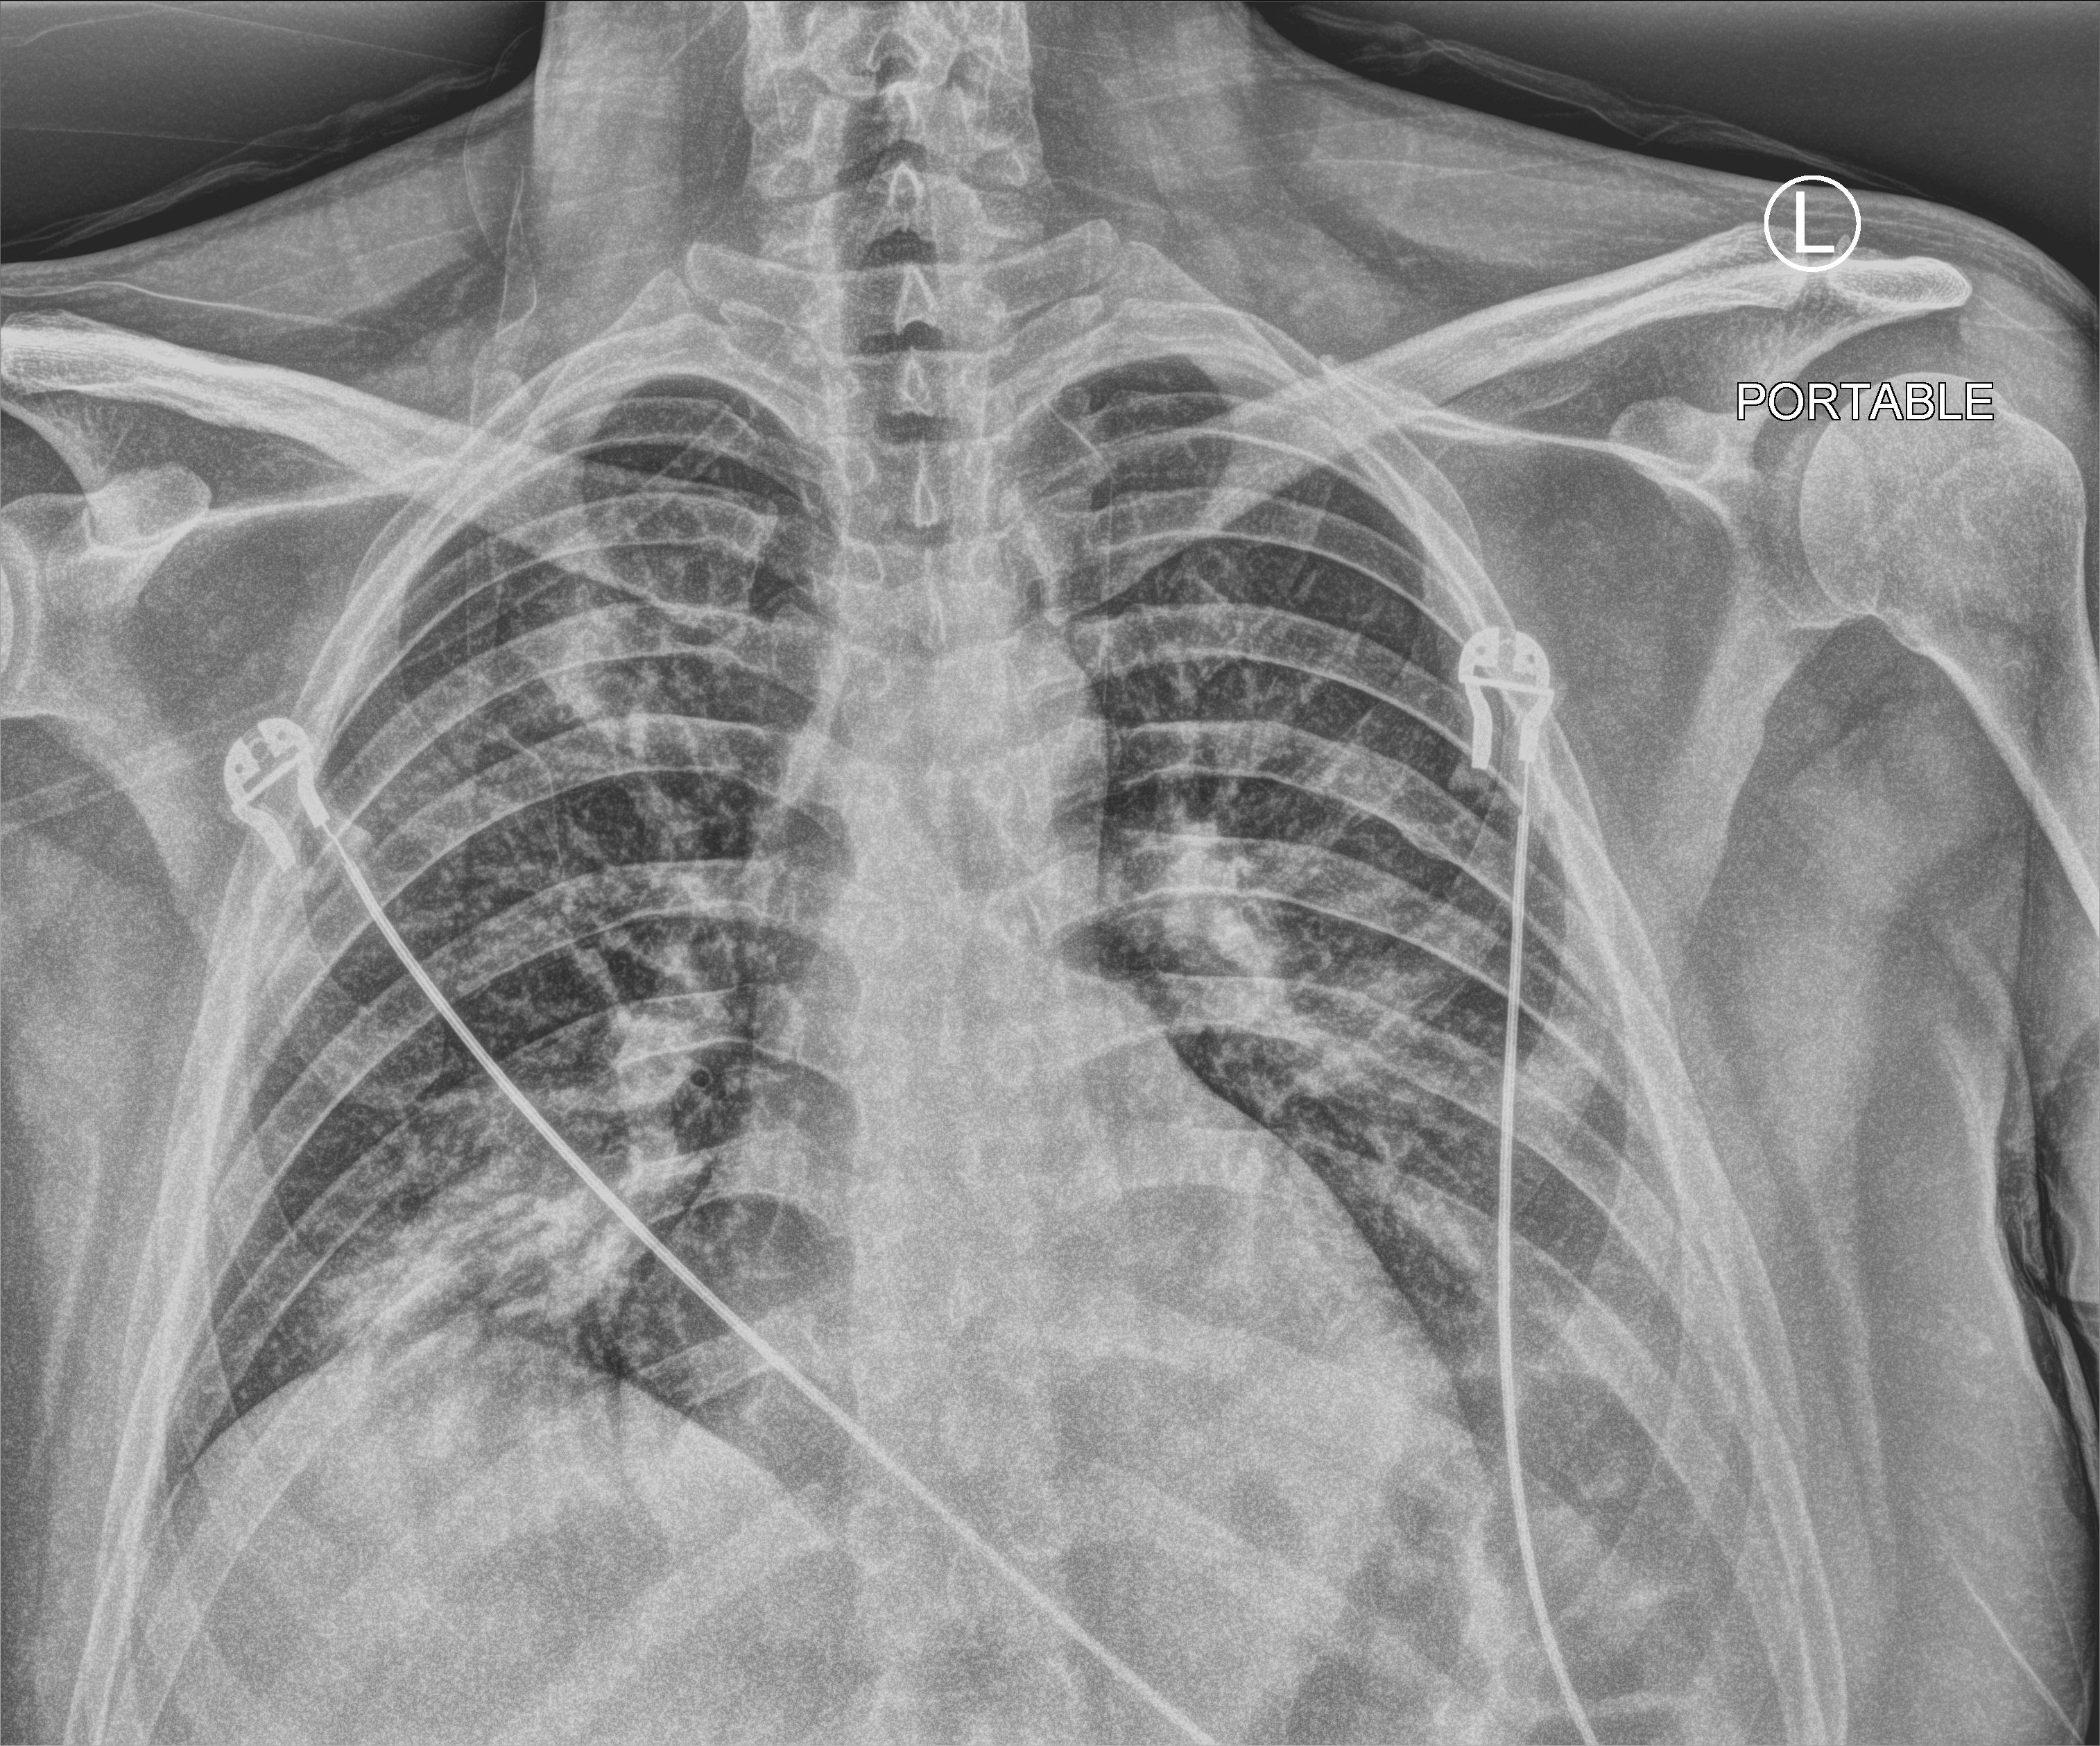
Portable chest radiograph. Male patient hospitalised with COVID-19, age 18–59 years.
From the hospital-stay record, not from the radiograph (when in the stay this image was taken is not recorded): mechanically ventilated during this hospital stay: no; admitted to intensive care during this hospital stay: no; diabetes (admission record): no.